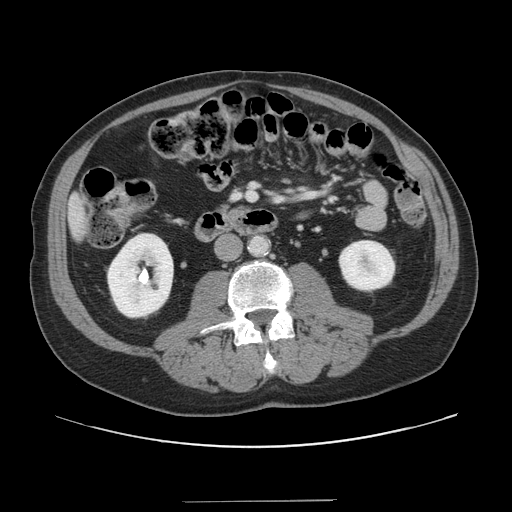
Contrast-enhanced abdominal CT, one axial slice. Position 36 of 151 along the scan axis. 120 kVp. Intravenous contrast given. Soft-tissue window (W 400 / L 40 HU). 2.5 mm slice thickness. 512 × 512 image matrix, field of view 399 × 399 mm. Male patient, age 63 years. From the clinical record (not read from this slice): diagnosis: colorectal cancer liver metastases, imaged before liver resection; multiple liver metastases: no; largest metastasis: 2.1 cm; disease in both lobes: no.
Annotated regions visible in this slice (manually delineated by an expert):
- liver: bounding box <70,197,86,237> (left, top, right, bottom; pixels)
- planned liver remnant (the part of the liver to remain after resection): <70,196,86,237>
- portal vein (with intrahepatic branches): <235,192,256,200>